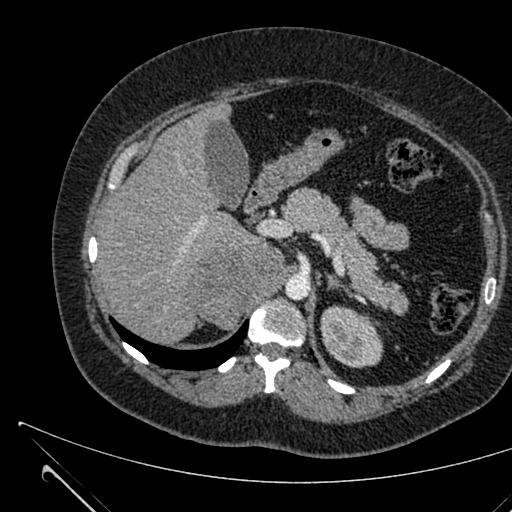
Contrast-enhanced abdominal CT, one axial slice; position 442 of 731 along the scan axis; intravenous contrast given; soft-tissue window (W 400 / L 40 HU); 1 mm slice thickness; 512 × 512 image matrix, field of view 376 × 376 mm. Patient: female, 36 years. Case-level facts recorded for this patient, not image findings: diagnosis: adrenocortical carcinoma; tumour side: right adrenal; tumour size at pathology: 10 cm; Ki-67 index: 20 %; stage (as recorded): 4.
Structures marked on this image (semi-automatic segmentation, software-assisted and operator-edited):
- mass: bounding box <191,243,282,329> (left, top, right, bottom; pixels)